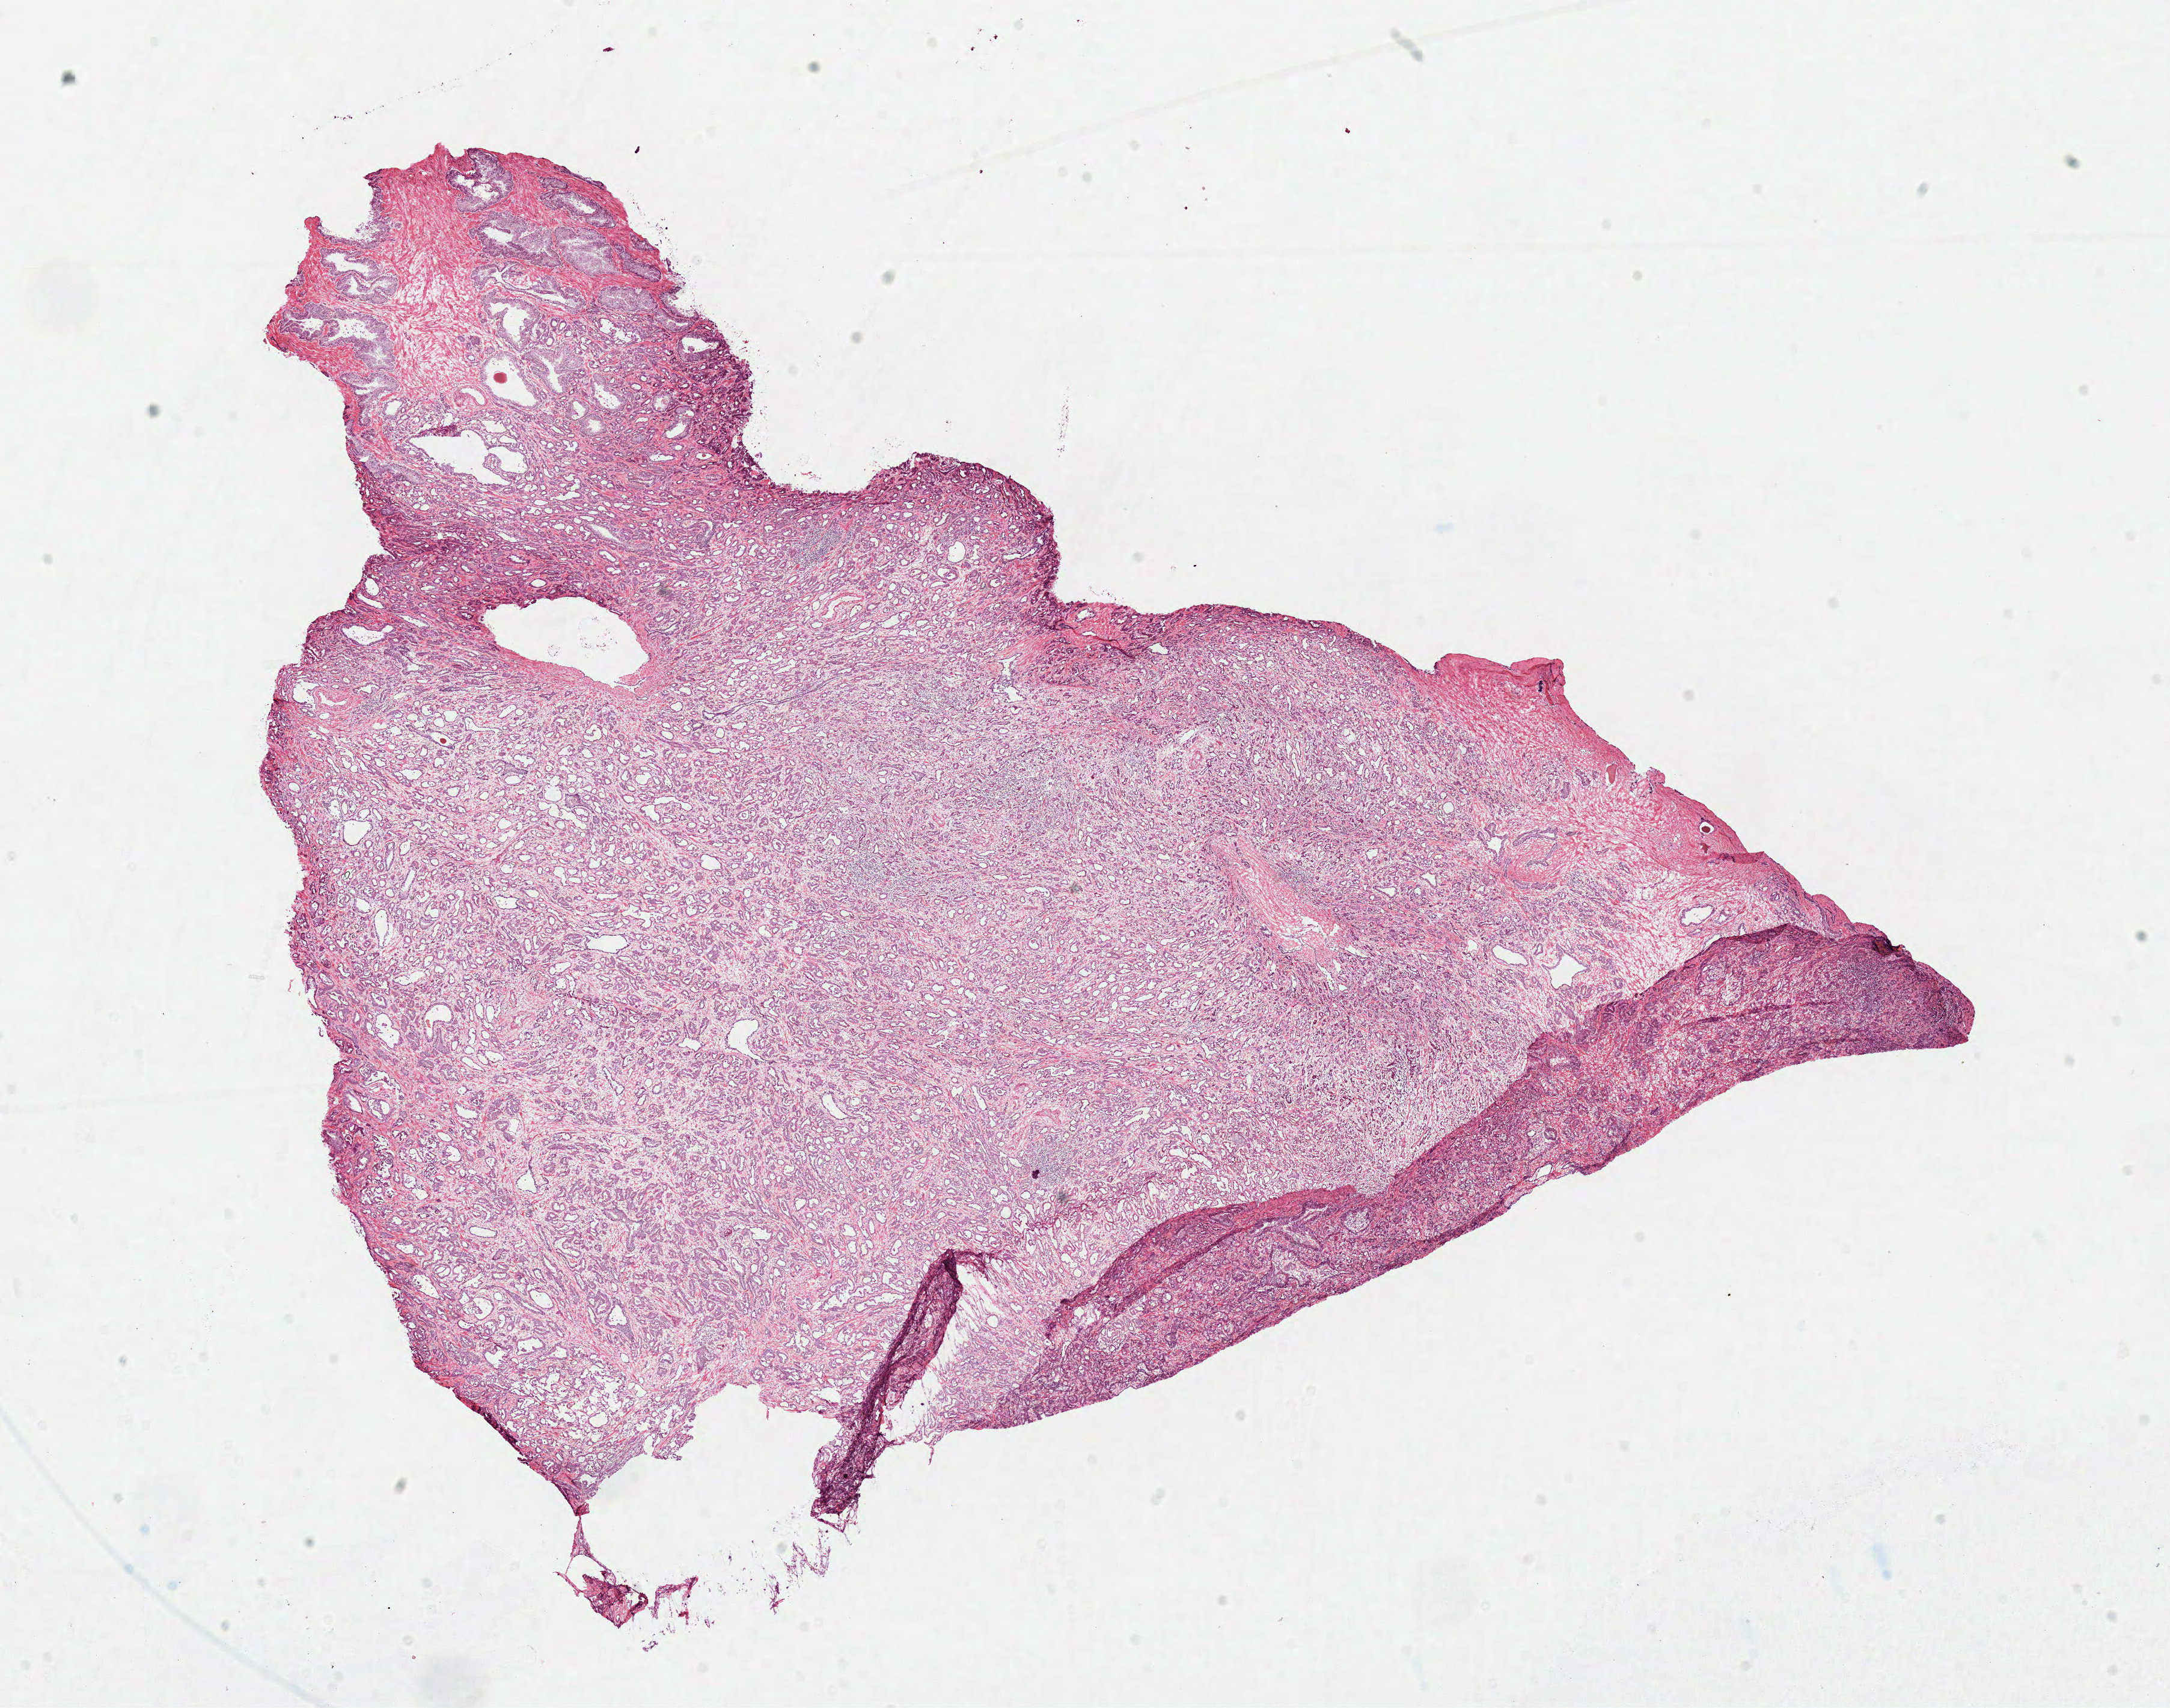
Digitized H&E tissue section (whole slide), shown as a low-resolution overview of the whole scanned area (about 14.2 x 11.2 mm), frozen section from the top of the tissue portion, primary tumour sample from the prostate. Male, age 53 years at initial diagnosis. Gleason score: 7 (3+4). Slide review estimates, as recorded: tumour cells 75%, tumour nuclei 80%, normal cells 12%, stromal cells 13%, necrosis 0%. Inflammatory infiltration, as recorded: lymphocyte infiltration 3%, monocyte infiltration 0%, neutrophil infiltration 0%.
Lymph nodes positive (case pathology): 0 of 14 examined. Histologic diagnosis: Acinar cell carcinoma.